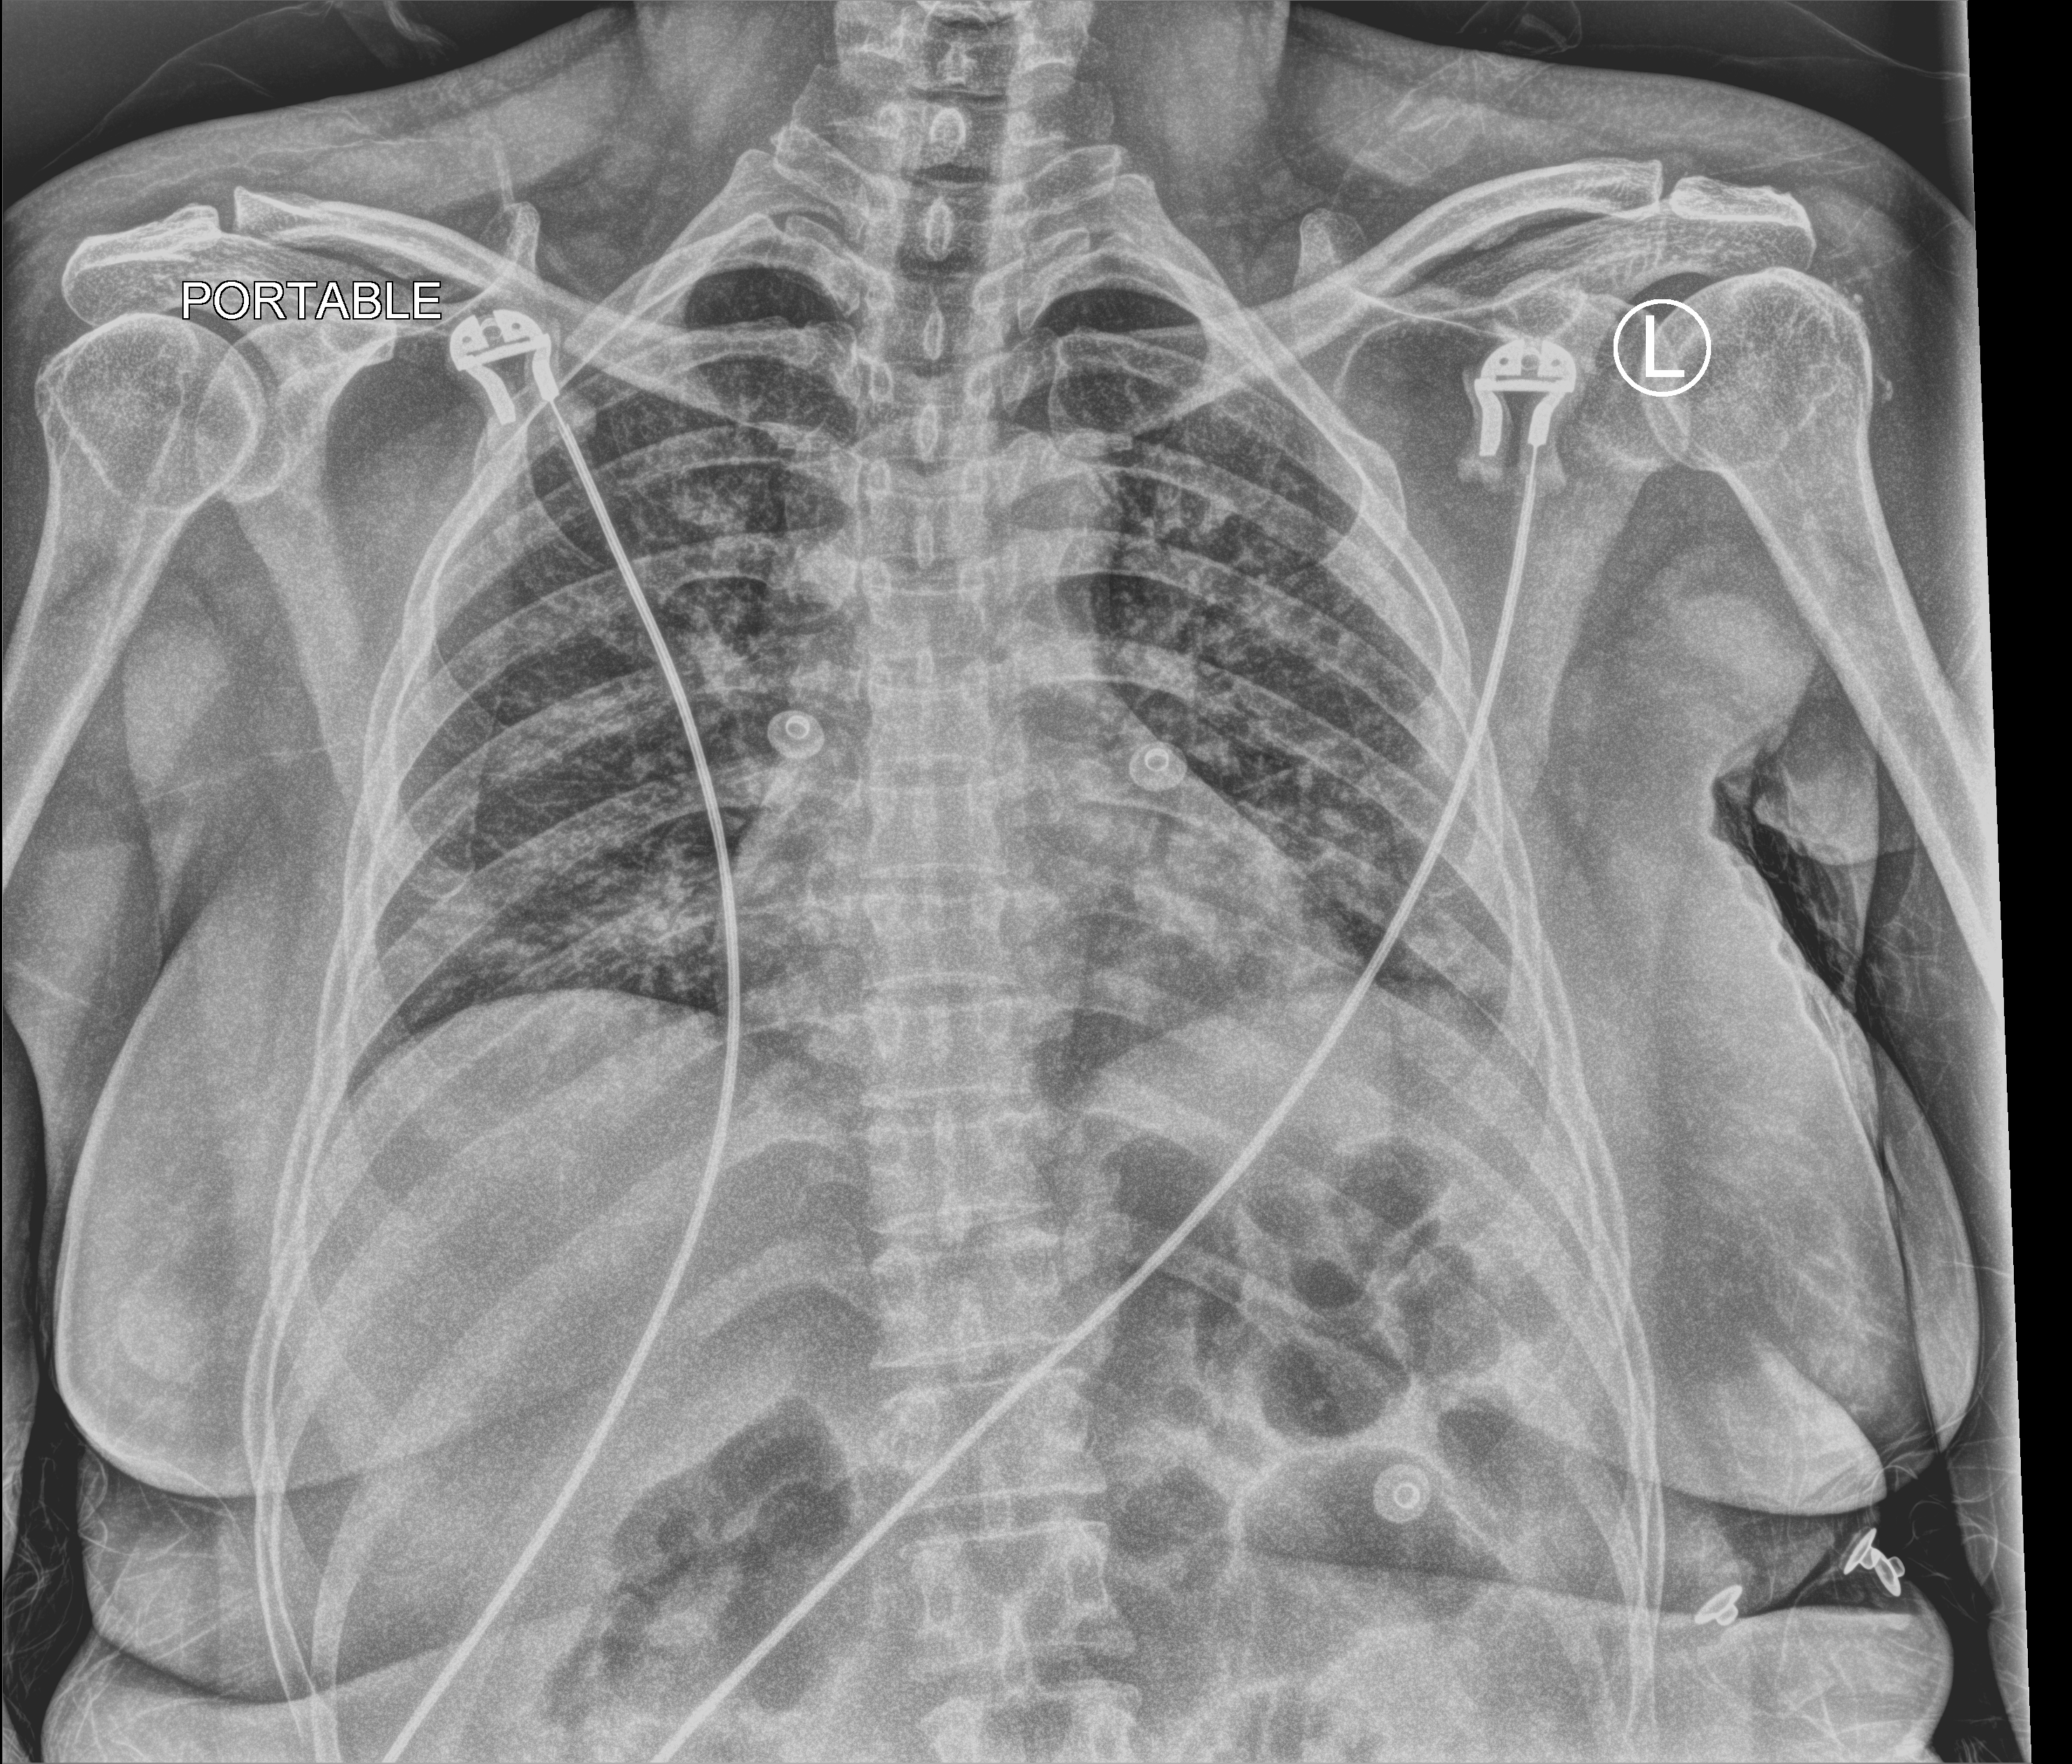
Portable chest radiograph, anteroposterior (AP) projection. Female patient hospitalised with COVID-19, age 18–59 years.
From the hospital-stay record, not from the radiograph (when in the stay this image was taken is not recorded): diabetes (admission record): no; length of hospital stay: 1 day.